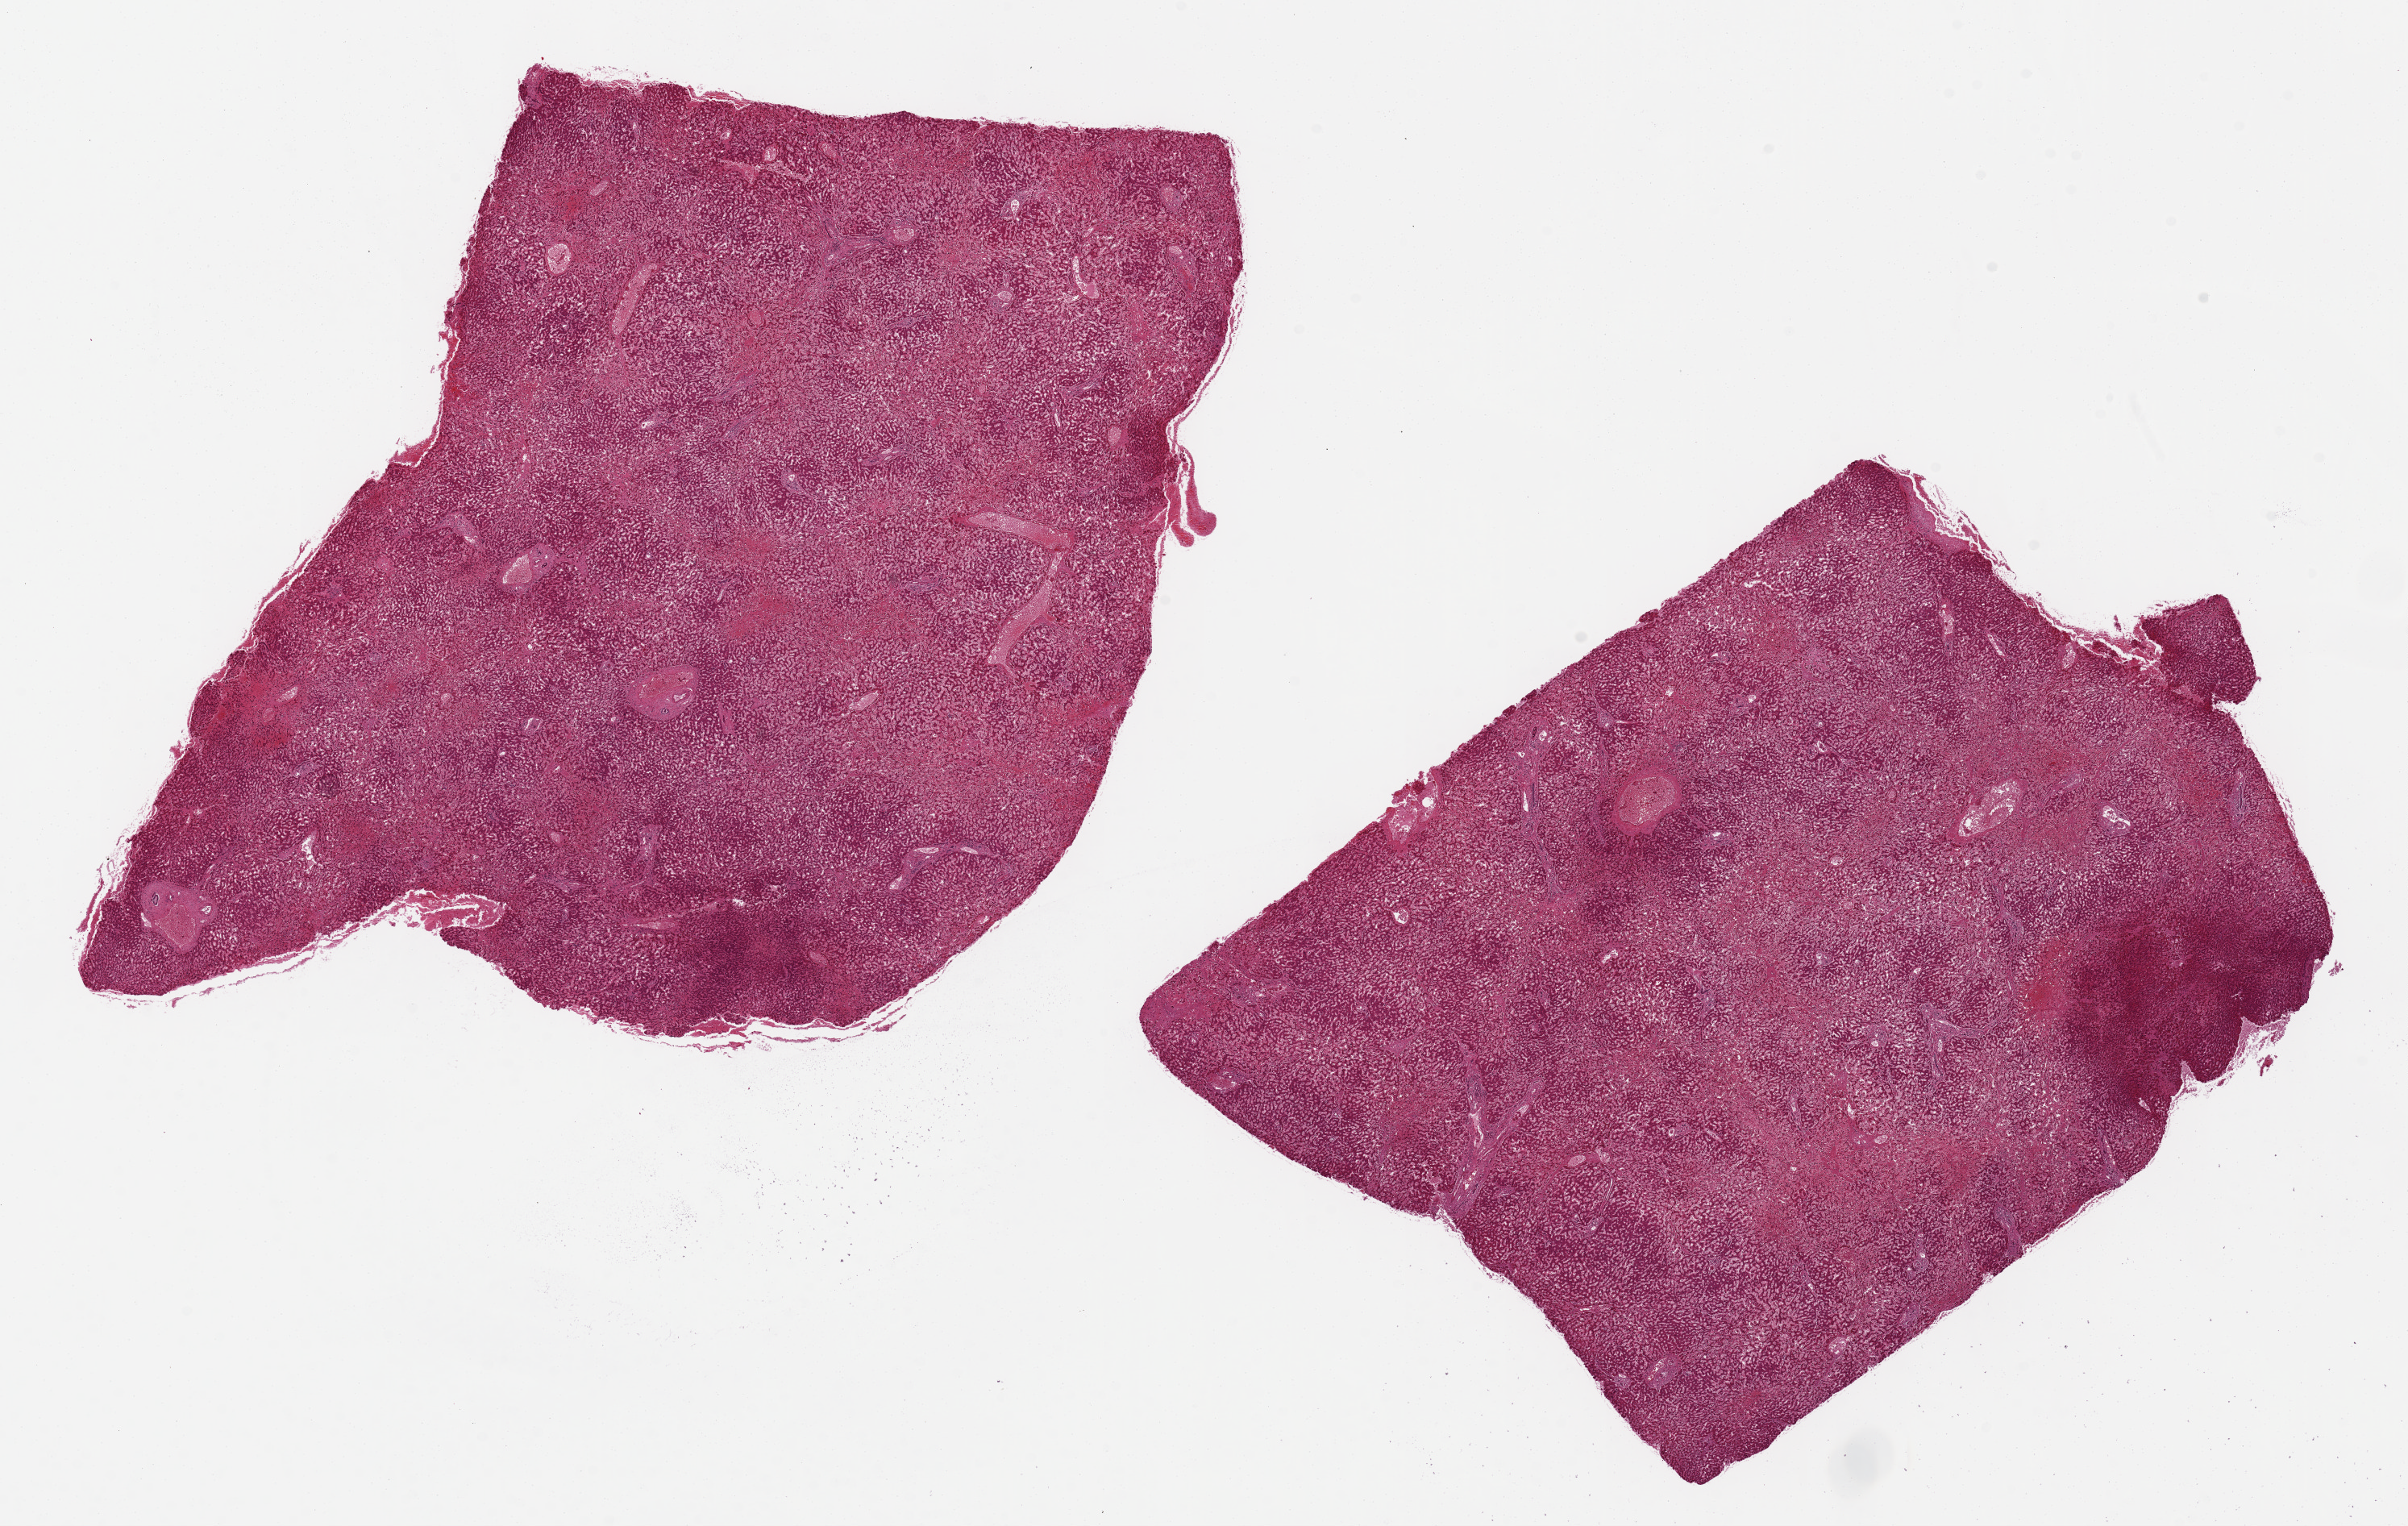
Whole-slide image, haematoxylin and eosin stain, a low-resolution overview of the entire scanned area, about 23.6 x 15.0 mm (from a 20x scan); PAXgene-fixed, paraffin-embedded tissue; target tissue: liver; tissue donor sample.
Reviewer comment on this tissue sample: 2 ~ 9x7mm aliquots.